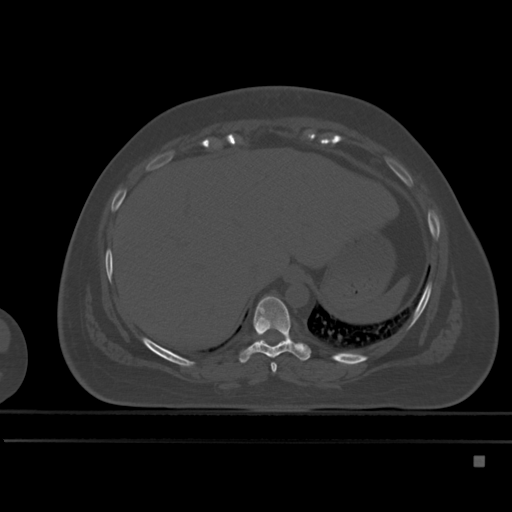
CT including the spine, one axial slice. Position 262 of 495 along the scan axis. Bone window (W 1800 / L 400 HU). 1.5 mm slice thickness. 512 × 512 image matrix, field of view 404 × 404 mm. Female patient, age 33 years. Case-level facts recorded for this patient, not image findings: primary cancer: breast; vertebrae with lytic lesions (as recorded): T1.
Annotated regions visible in this slice (semi-automatically segmented with operator editing):
- T10 vertebra: box from (x=257, y=337) to (x=290, y=341) px
- T8 vertebra: (x=271, y=362)–(x=277, y=373)
- T9 vertebra: (x=239, y=295)–(x=311, y=363)